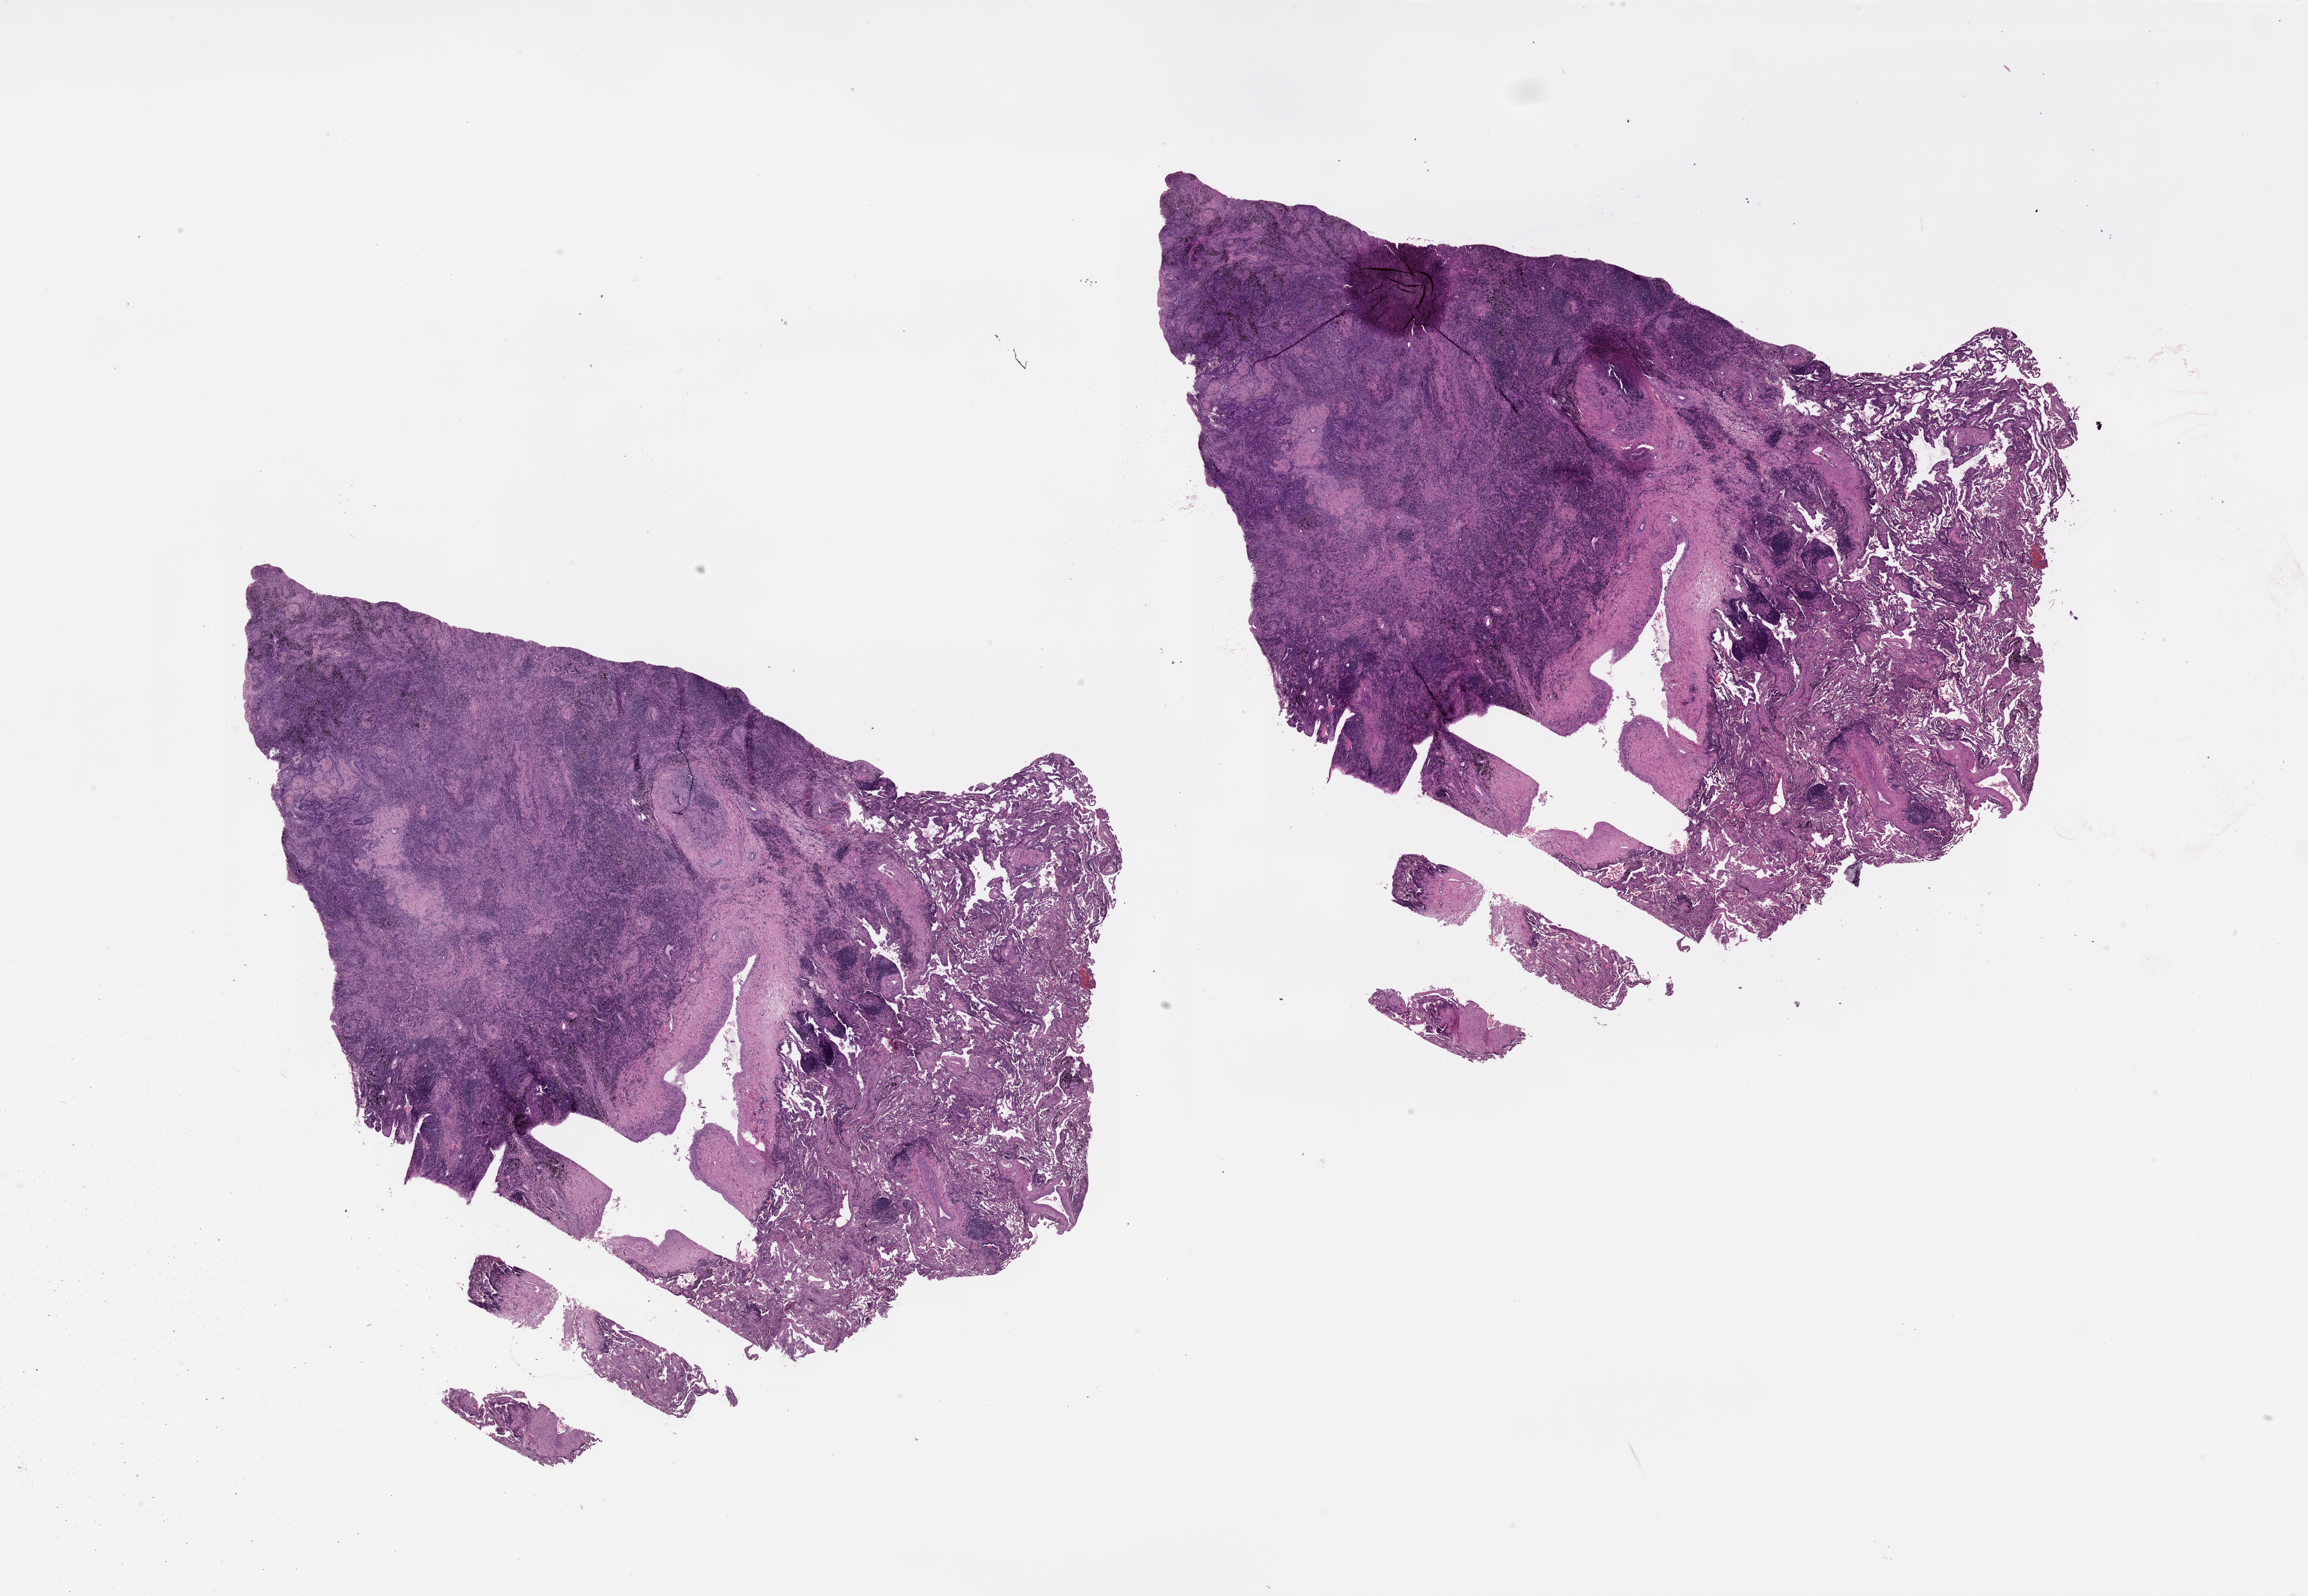
Whole-slide histology image, H&E-stained — low-resolution overview of the scanned area, about 31.1 x 21.5 mm (acquisition: 20x scan), tumour tissue sample, lung. Patient: male, age 66 years.
Patient diagnosis (cohort enrolment): squamous cell carcinoma (lung).